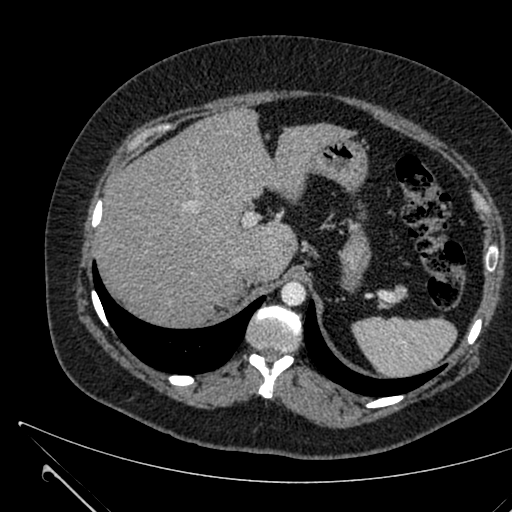
Contrast-enhanced abdominal CT, one axial slice. Slice 489 of 731 in the series (ordered by position). 120 kVp. Intravenous contrast given. Soft-tissue window (W 400 / L 40 HU). 512 × 512 image matrix, field of view 376 × 376 mm. Patient: female, 36 years. From the clinical record (not read from this slice): diagnosis: adrenocortical carcinoma; tumour side: right adrenal; tumour size at pathology: 10 cm; Ki-67 index: 20 %; stage (as recorded): 4.
Annotated regions visible in this slice (semi-automatically segmented with operator editing):
- mass: box from (x=223, y=280) to (x=243, y=305) px